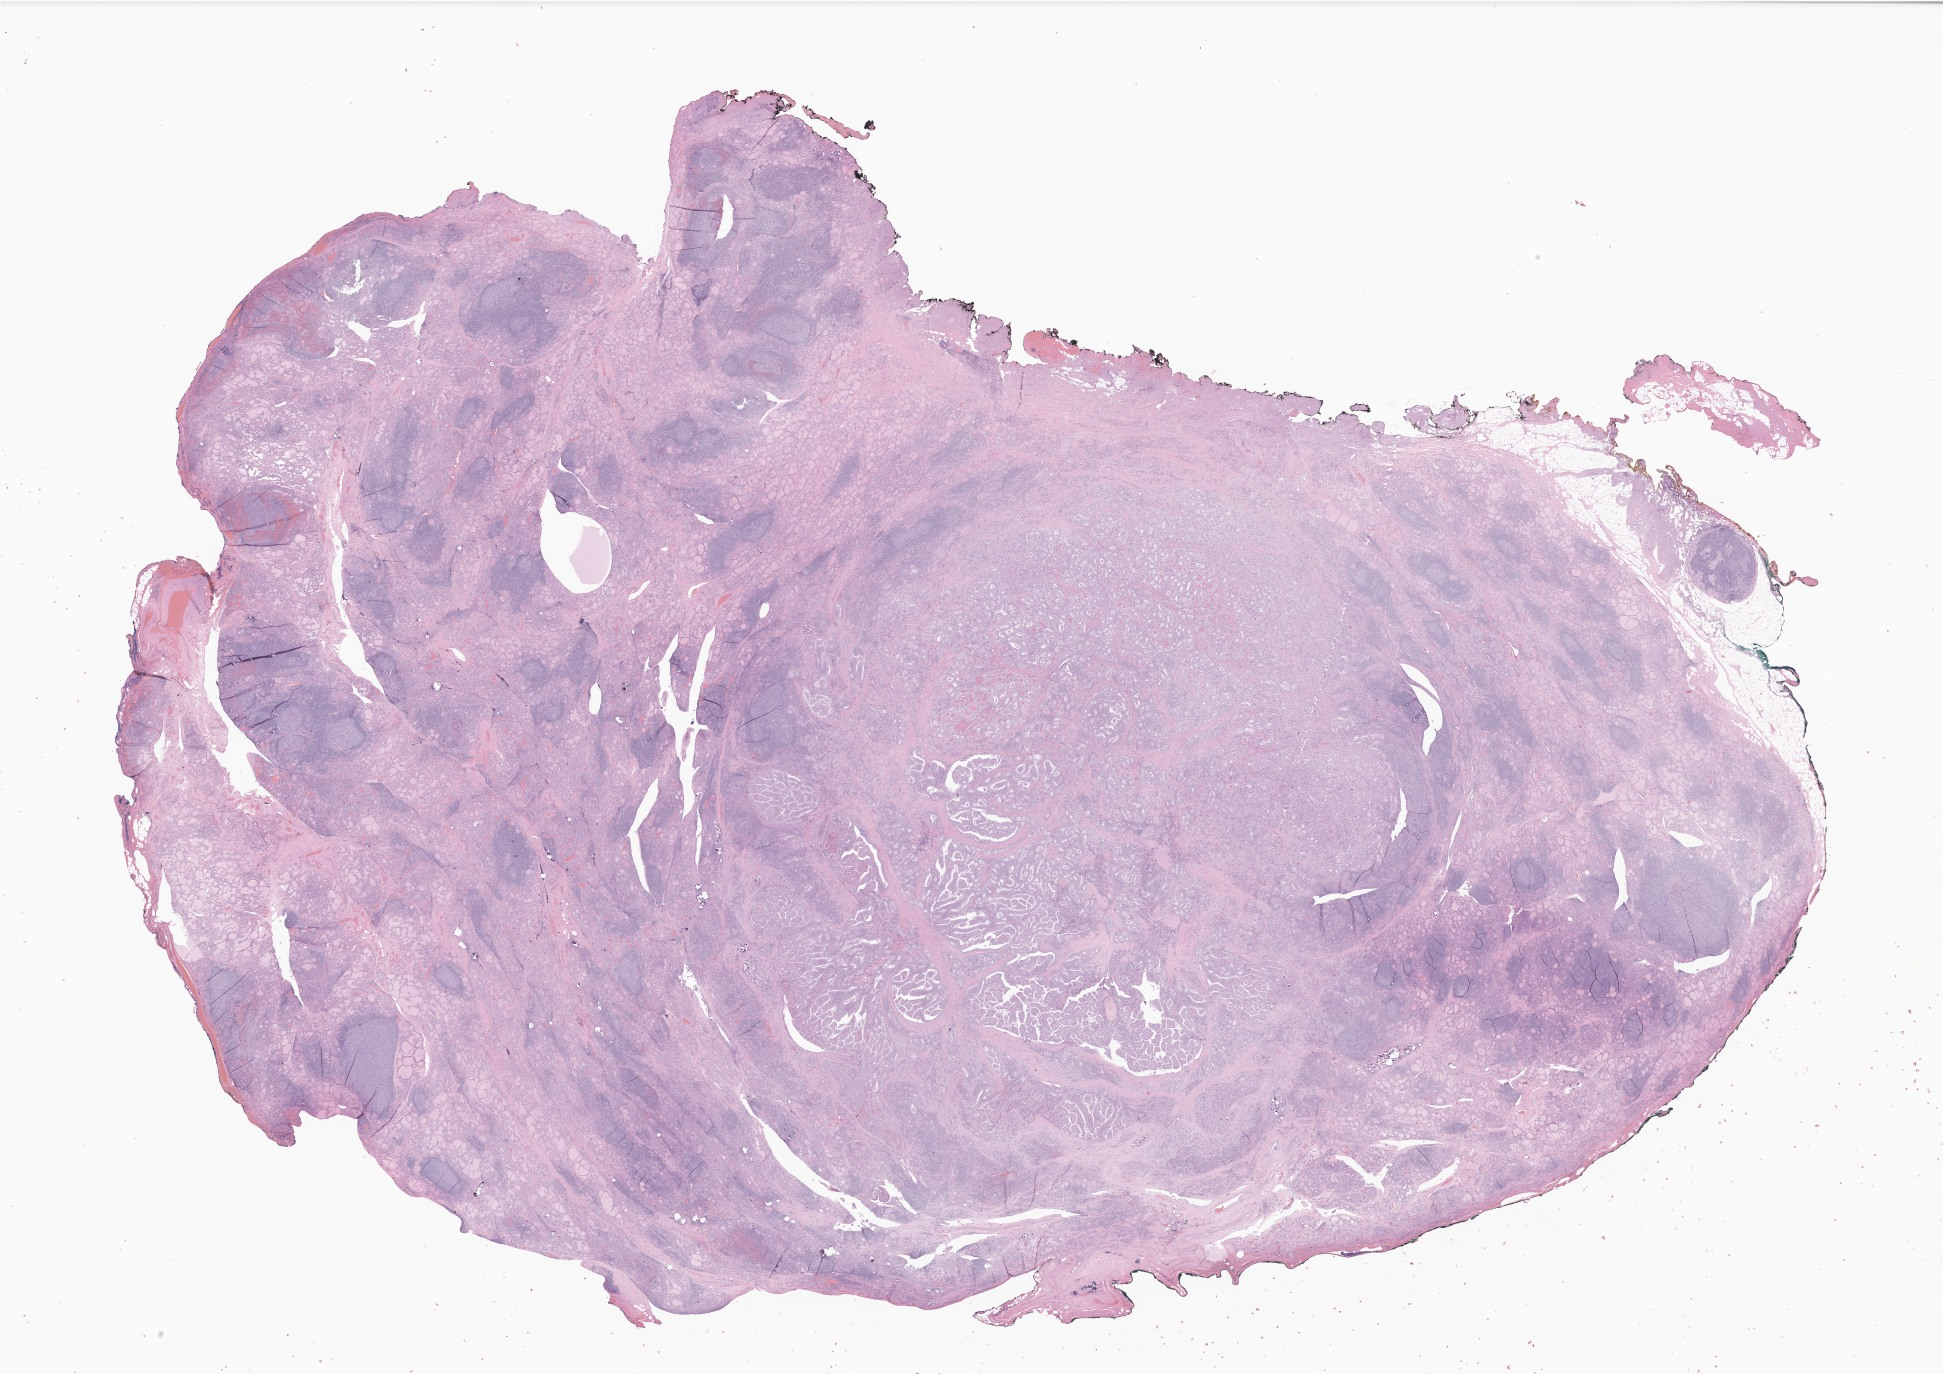
Whole-slide image, hematoxylin and eosin (H&E) stain of tumor tissue from the thyroid — a low-resolution overview of the entire scanned area, about 32.8 x 23.2 mm. Formalin-fixed, paraffin-embedded (FFPE) tissue. Patient: male, age 186 months (15 years 6 months).
Diagnosis: Papillary carcinoma, NOS.